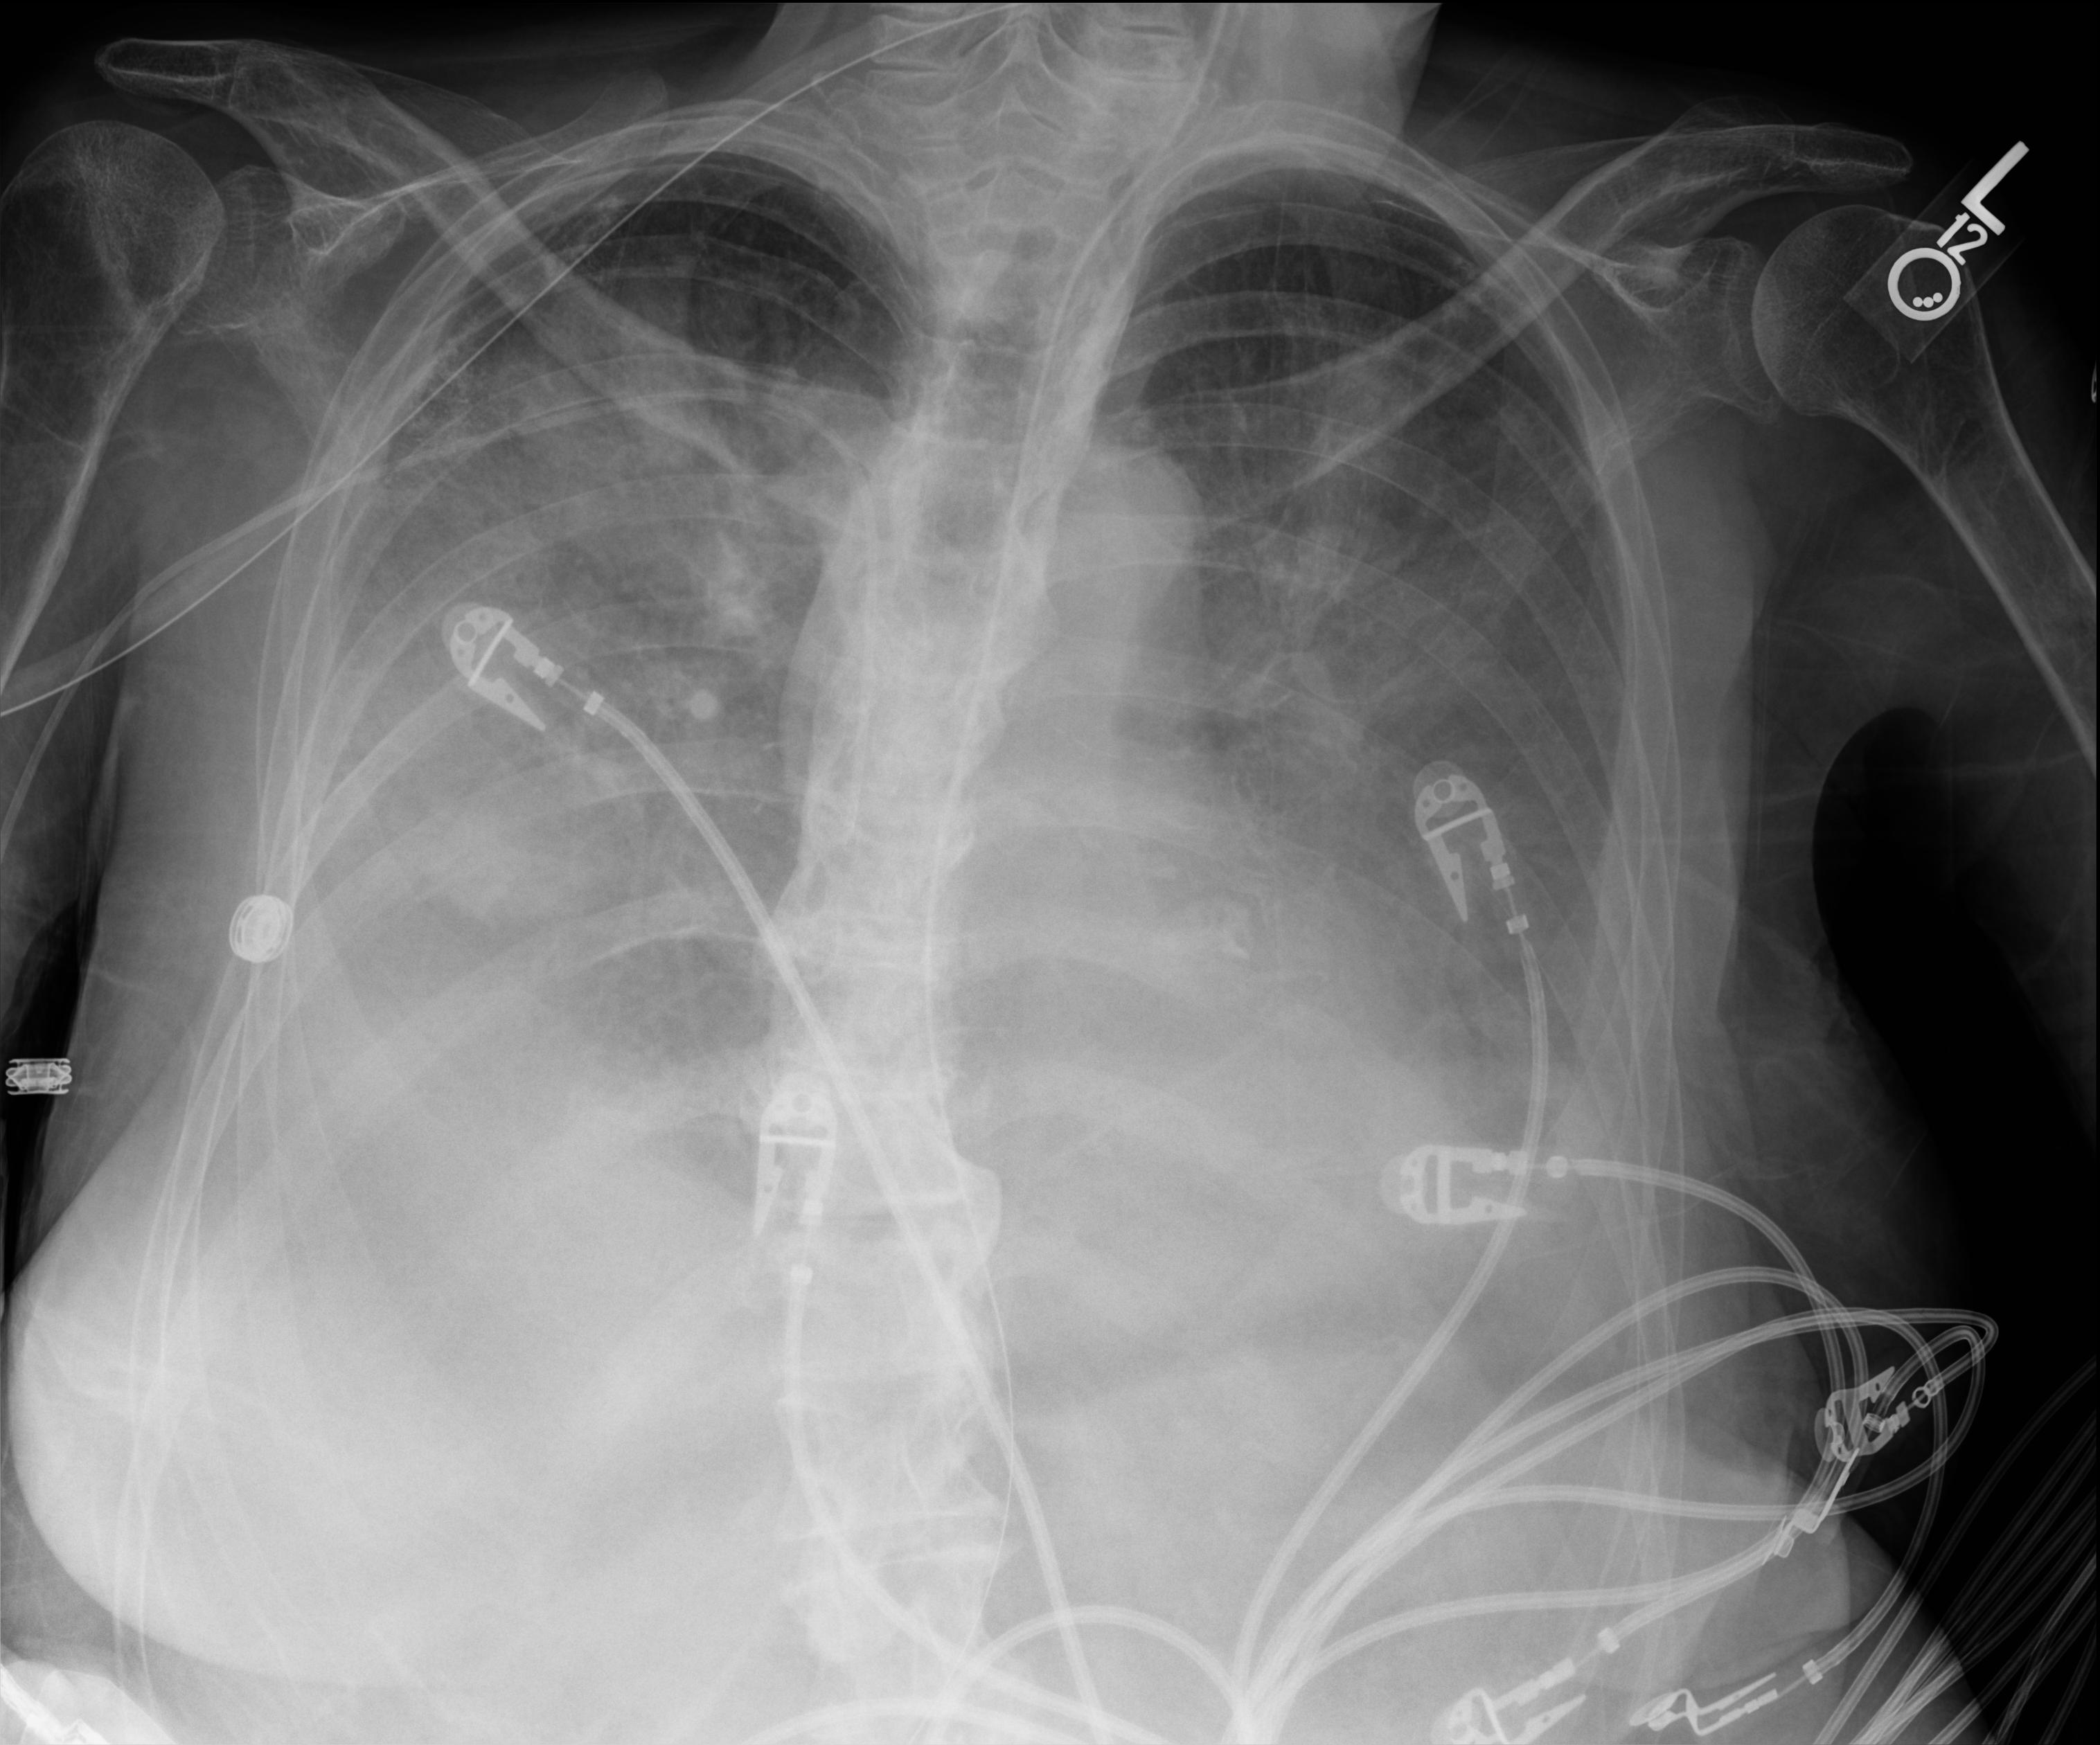
Bedside chest radiograph (digital radiography), anteroposterior (AP) projection. Patient hospitalised with COVID-19; female, aged 60–74 years.
From the hospital-stay record, not from the radiograph (when in the stay this image was taken is not recorded): mechanically ventilated during this hospital stay: no; hypertension (admission record): no.